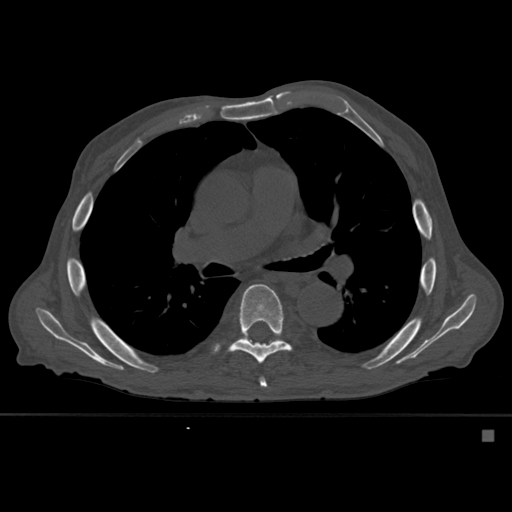
CT including the spine, one axial slice. Slice 369 of 527 in the series (ordered by position). Bone window (W 1800 / L 400 HU). 1.5 mm slice thickness. 512 × 512 image matrix. Male patient, age 78 years. Case-level facts recorded for this patient, not image findings: primary cancer: prostate.
Outlined on this slice (semi-automatically segmented with operator editing):
- T6 vertebra: bounding box <259,377,267,388> (left, top, right, bottom; pixels)
- T7 vertebra: <213,284,292,364>